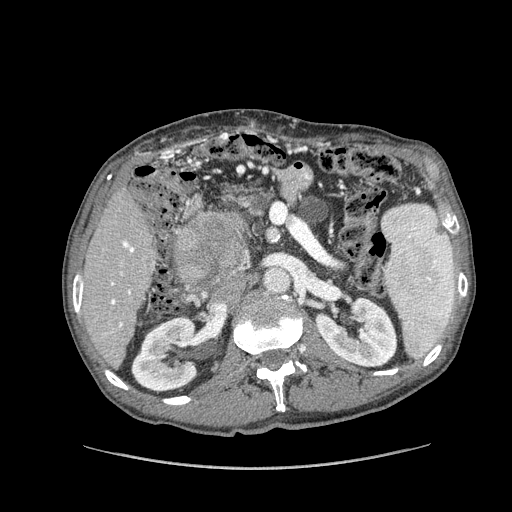
Contrast-enhanced abdominal CT (liver protocol), one axial slice; slice 49 of 162 in the series (ordered by position); reconstruction kernel STANDARD; soft-tissue window (W 400 / L 40 HU); 512 × 512 image matrix. From the clinical record (not read from this slice): diagnosis: hepatocellular carcinoma (patient treated with transarterial chemoembolisation; whether this scan precedes or follows treatment is not stated here); TNM stage (as recorded): Stage-IIIA; Child-Pugh class: A; tumour nodularity: multinodular.
Structures marked on this image (semi-automatic segmentation, software-assisted and operator-edited):
- liver parenchyma outside the tumour (the mass and vessels are separate outlines, so this box may not span the whole liver): bounding box (x1, y1, x2, y2) in pixels: (81, 184, 158, 366)
- mass: (174, 211, 244, 286)
- liver vessels: (111, 241, 134, 327)